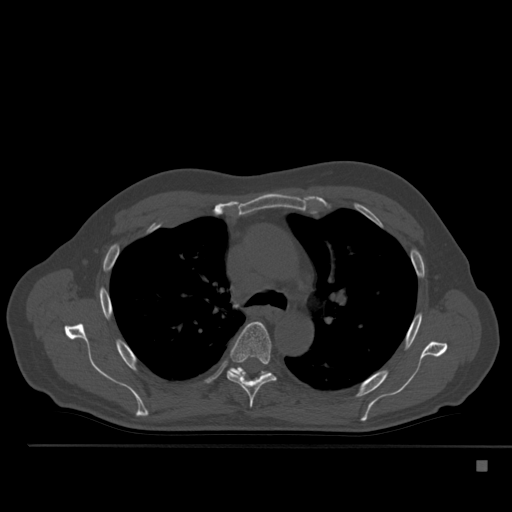
CT including the spine, one axial slice; position 363 of 517 along the scan axis; 120 kVp; bone window (W 1800 / L 400 HU); 512 × 512 image matrix. Patient: male, 70 years. Case-level facts recorded for this patient, not image findings: primary cancer: renal; vertebrae with lytic lesions (as recorded): T4, T6, T10, T12, L3, L4, L5.
Annotated regions visible in this slice (semi-automatic segmentation, software-assisted and operator-edited):
- T5 vertebra: bounding box <227,322,276,408> (left, top, right, bottom; pixels)
- T6 vertebra: <228,367,268,380>